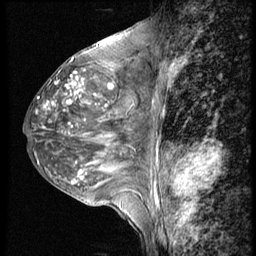
Breast MRI (dynamic contrast-enhanced), one sagittal slice. Position 24 of 56 along the scan axis. 4 images stored at this slice position (order not interpretable as contrast timing). 1.5 T. TE 4.2 ms, TR 9 ms. 2.5 mm slice thickness. 256 × 256 image matrix, field of view 180 × 180 mm. Female patient, age 50 years. Case-level facts recorded for this patient, not image findings: setting: breast cancer imaged before/during neoadjuvant chemotherapy; receptor status: triple-negative.
Annotated regions visible in this slice (semi-automatically segmented with operator editing):
- analysis volume of interest (the breast-tissue region the enhancement analysis was run in; not a lesion): bounding box [x1, y1, x2, y2] px = [22, 46, 148, 188]
- tumour enhancement mask (voxels above the 140 % enhancement threshold inside the analysis volume of interest): [43, 72, 114, 184]